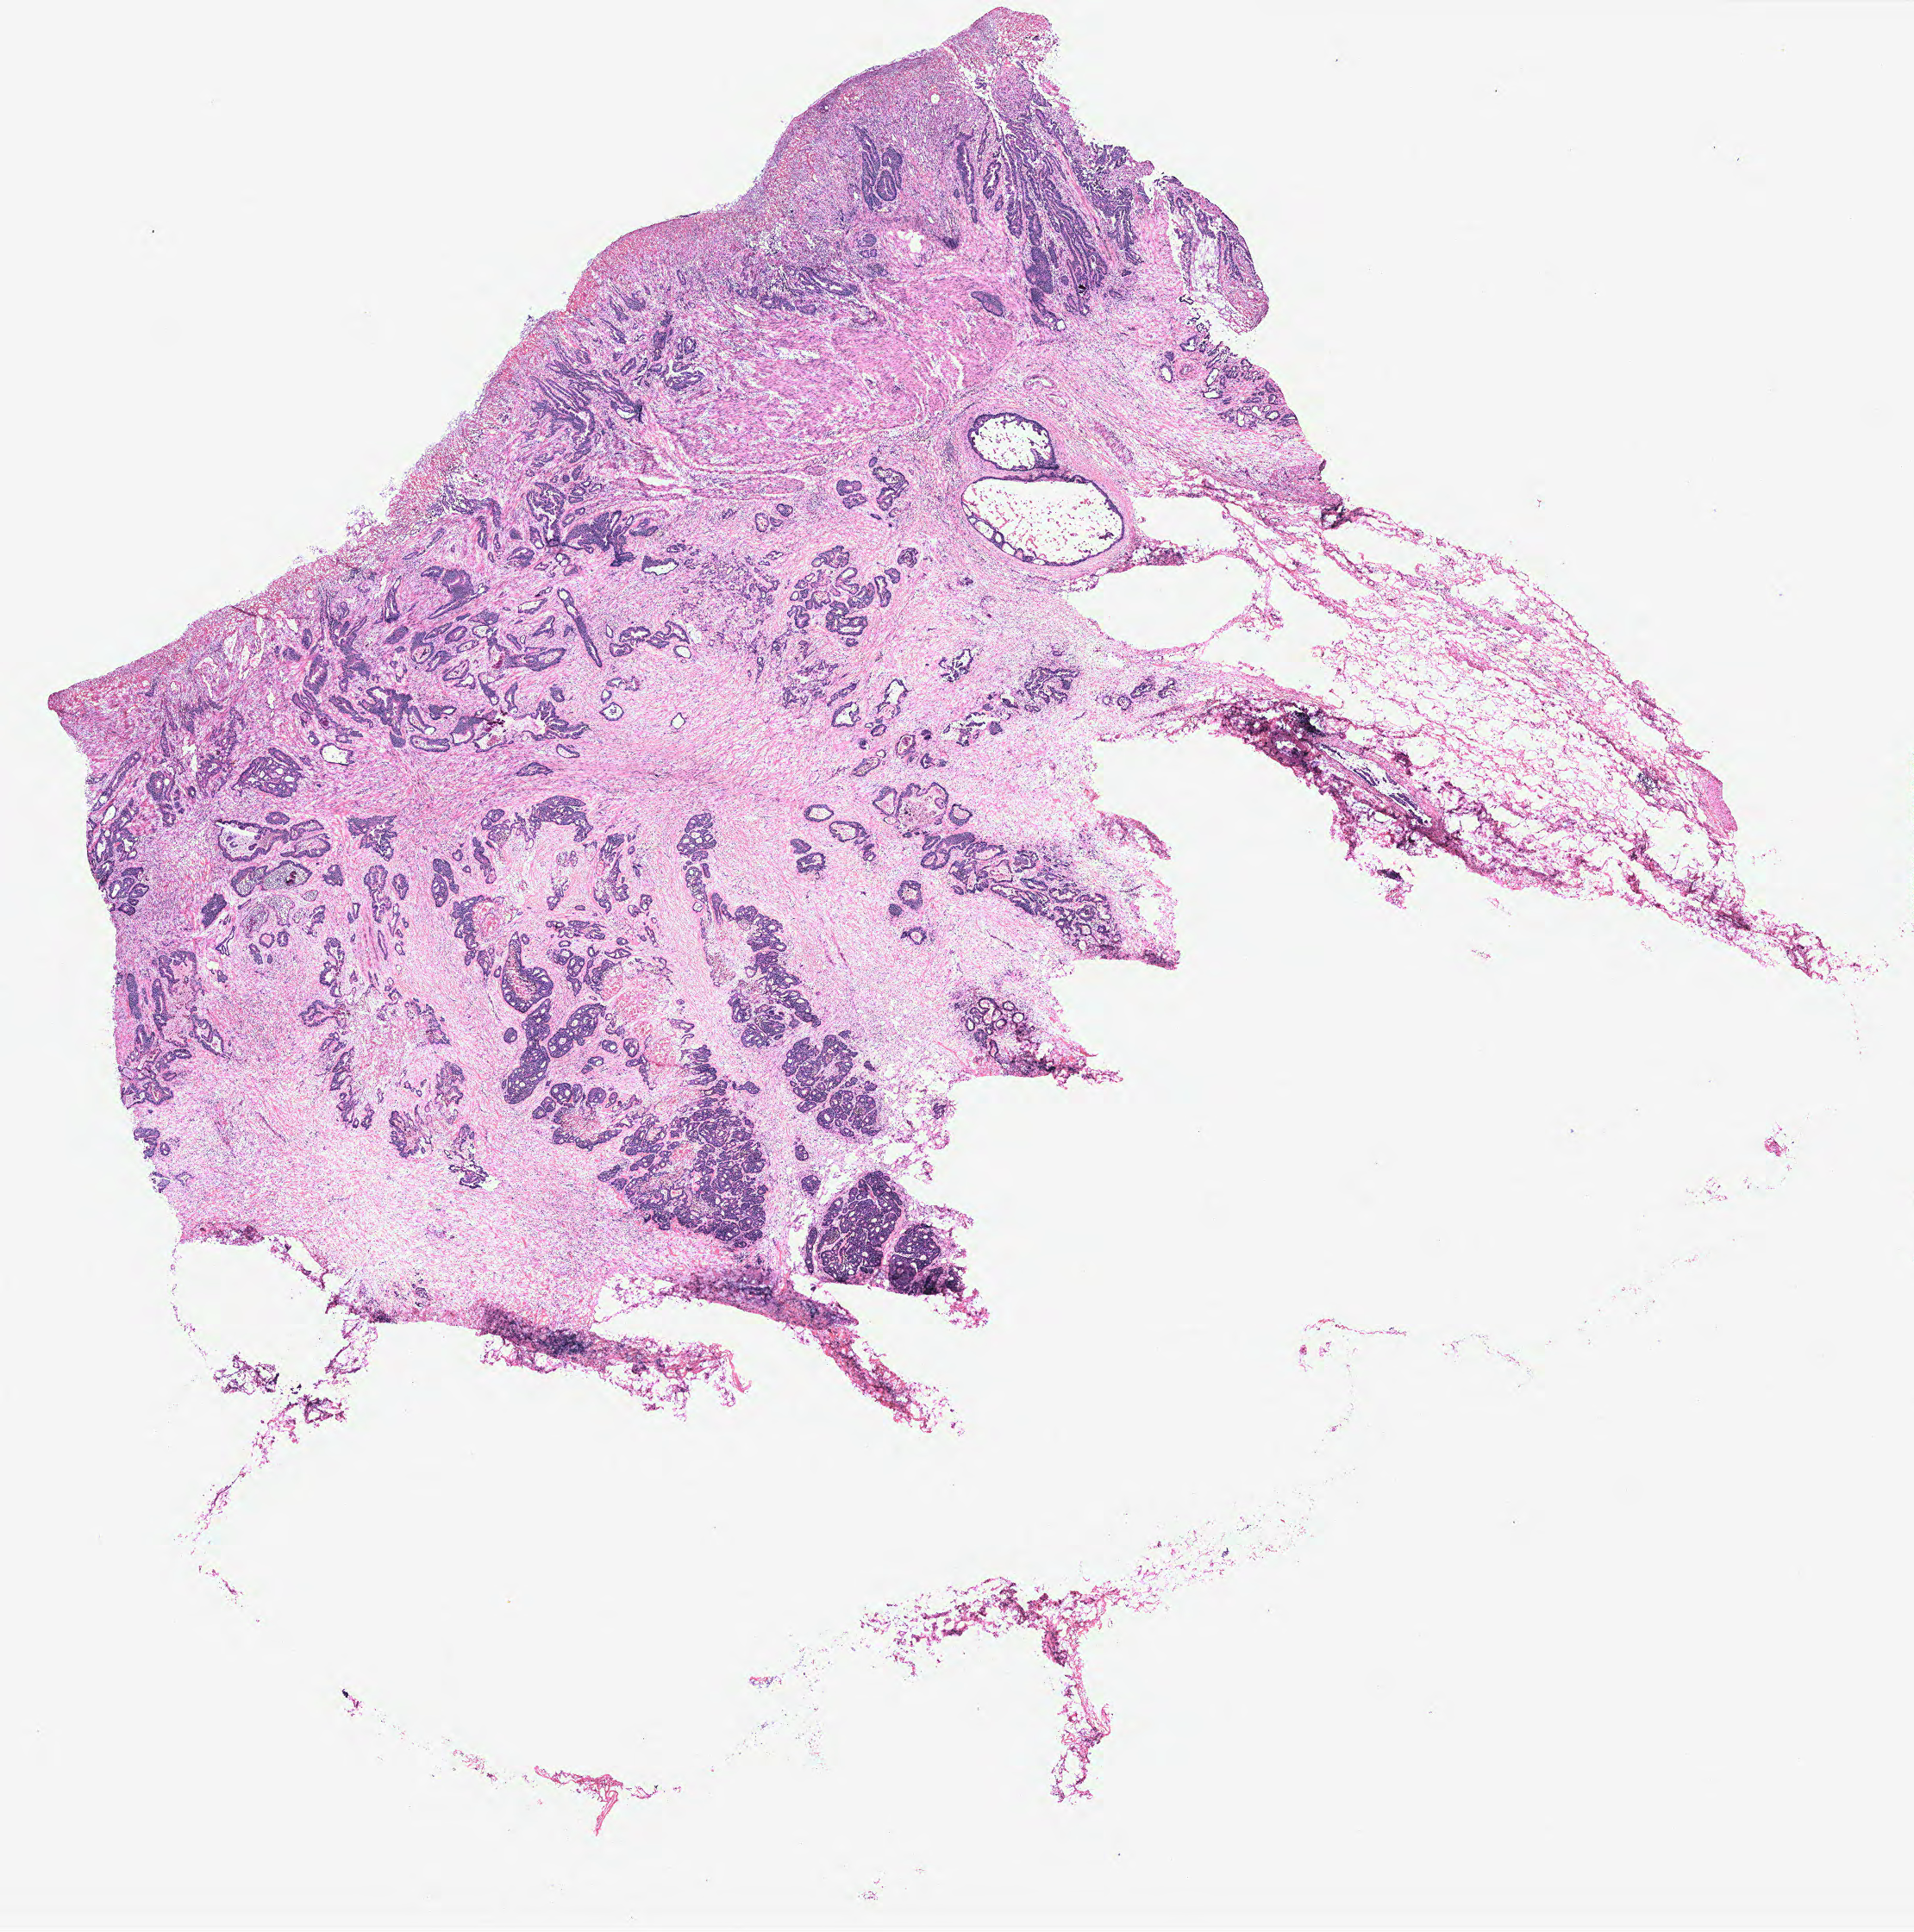
Hematoxylin and eosin (H&E) stained whole-slide image, a low-resolution overview of the entire scanned area, about 17.8 x 17.9 mm. Colon, tissue type not recorded.
Patient diagnosis (cohort enrolment): colon cancer (colon).